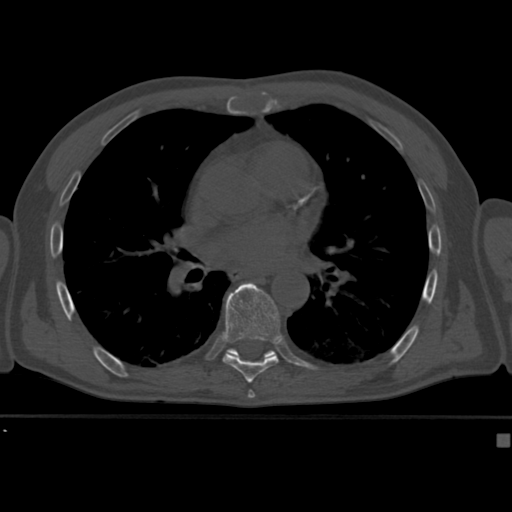
CT including the spine, one axial slice; position 260 of 430 along the scan axis; reconstruction kernel Br40s; 120 kVp; bone window (W 1800 / L 400 HU); 512 × 512 image matrix. Male patient, age 64 years. From the clinical record (not read from this slice): primary cancer: uterus; vertebrae with lytic lesions (as recorded): T1, T4, T5, T7, L5.
Annotated regions visible in this slice (semi-automatic segmentation, software-assisted and operator-edited):
- T8 vertebra: bounding box (x1, y1, x2, y2) in pixels: (223, 282, 280, 382)
- T9 vertebra: (226, 348, 280, 359)